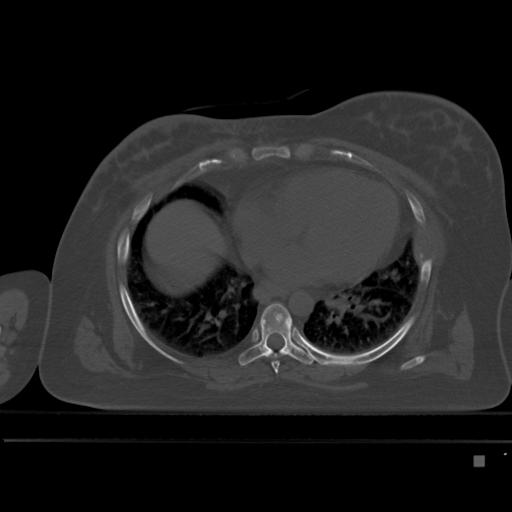
CT including the spine, one axial slice. Position 295 of 495 along the scan axis. Bone window (W 1800 / L 400 HU). 1.5 mm slice thickness. 512 × 512 image matrix, field of view 404 × 404 mm. Patient: female, 33 years. From the clinical record (not read from this slice): primary cancer: breast; vertebrae with lytic lesions (as recorded): T1.
Structures marked on this image (semi-automatically segmented with operator editing):
- T6 vertebra: box from (x=272, y=361) to (x=279, y=373) px
- T7 vertebra: (x=239, y=303)–(x=316, y=366)